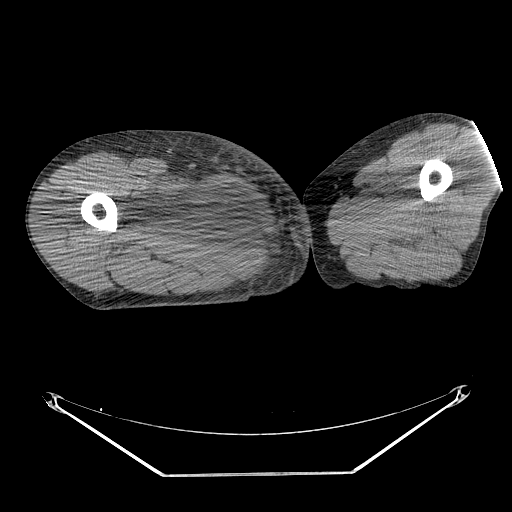
CT of an extremity soft-tissue mass (from a PET/CT study), one axial slice. Slice 244 of 311 in the series (ordered by position). Soft-tissue window (W 400 / L 40 HU). 3.75 mm slice thickness. 512 × 512 image matrix, field of view 500 × 500 mm. Male patient. From the clinical record (not read from this slice): histological type: undifferentiated - pleiomorphic; grade: high; site of the primary tumour: right thigh.
Structures marked on this image (expert contour drawn on MRI and transferred to this co-registered scan by the dataset authors):
- gross tumour volume including surrounding oedema: bounding box (x1, y1, x2, y2) in pixels: (128, 178, 232, 252)
- gross tumour volume (mass): (162, 183, 232, 248)